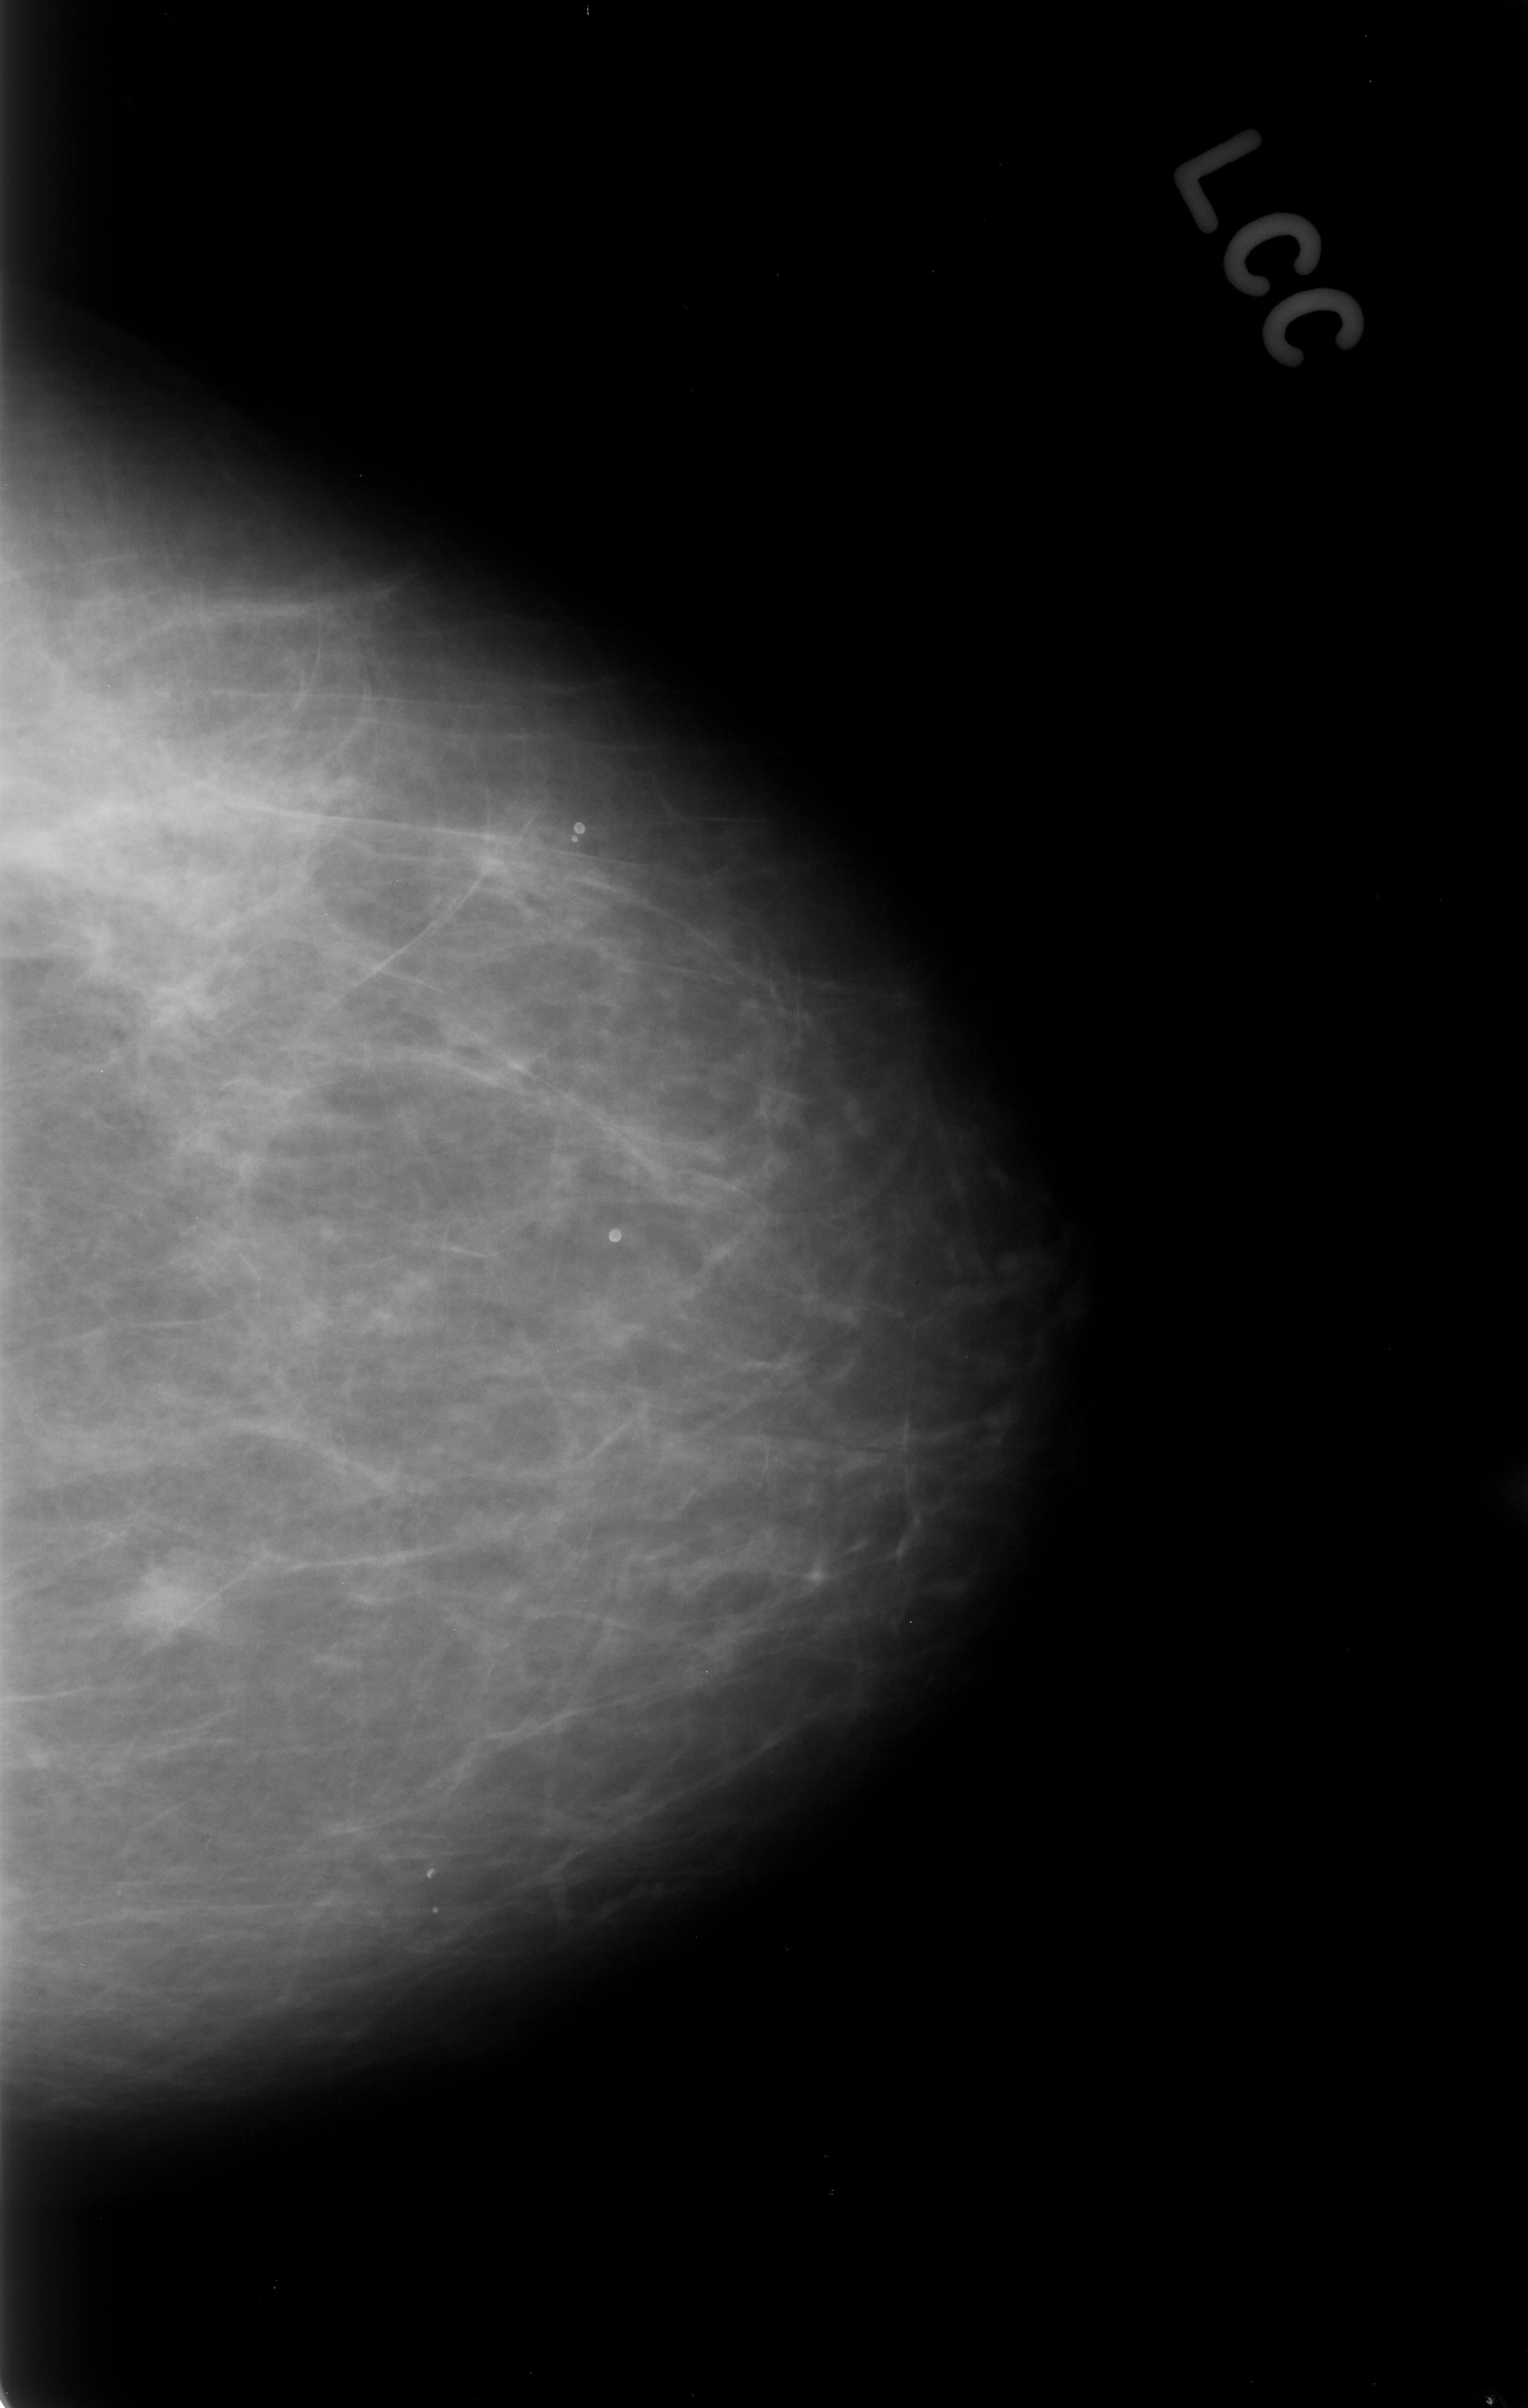
Digitized screen-film mammogram; left breast; craniocaudal (CC) view; BI-RADS breast density category 1 (scale 1–4); 1528 × 2408 image matrix.
Expert-marked regions of interest on this image (one box per marked abnormality):
- mass, shape irregular, margins microlobulated; BI-RADS assessment category 3; benign; no additional work-up was recommended (outcome (as recorded, no biopsy): benign without callback): bounding box [x1, y1, x2, y2] px = [99, 1545, 245, 1657]